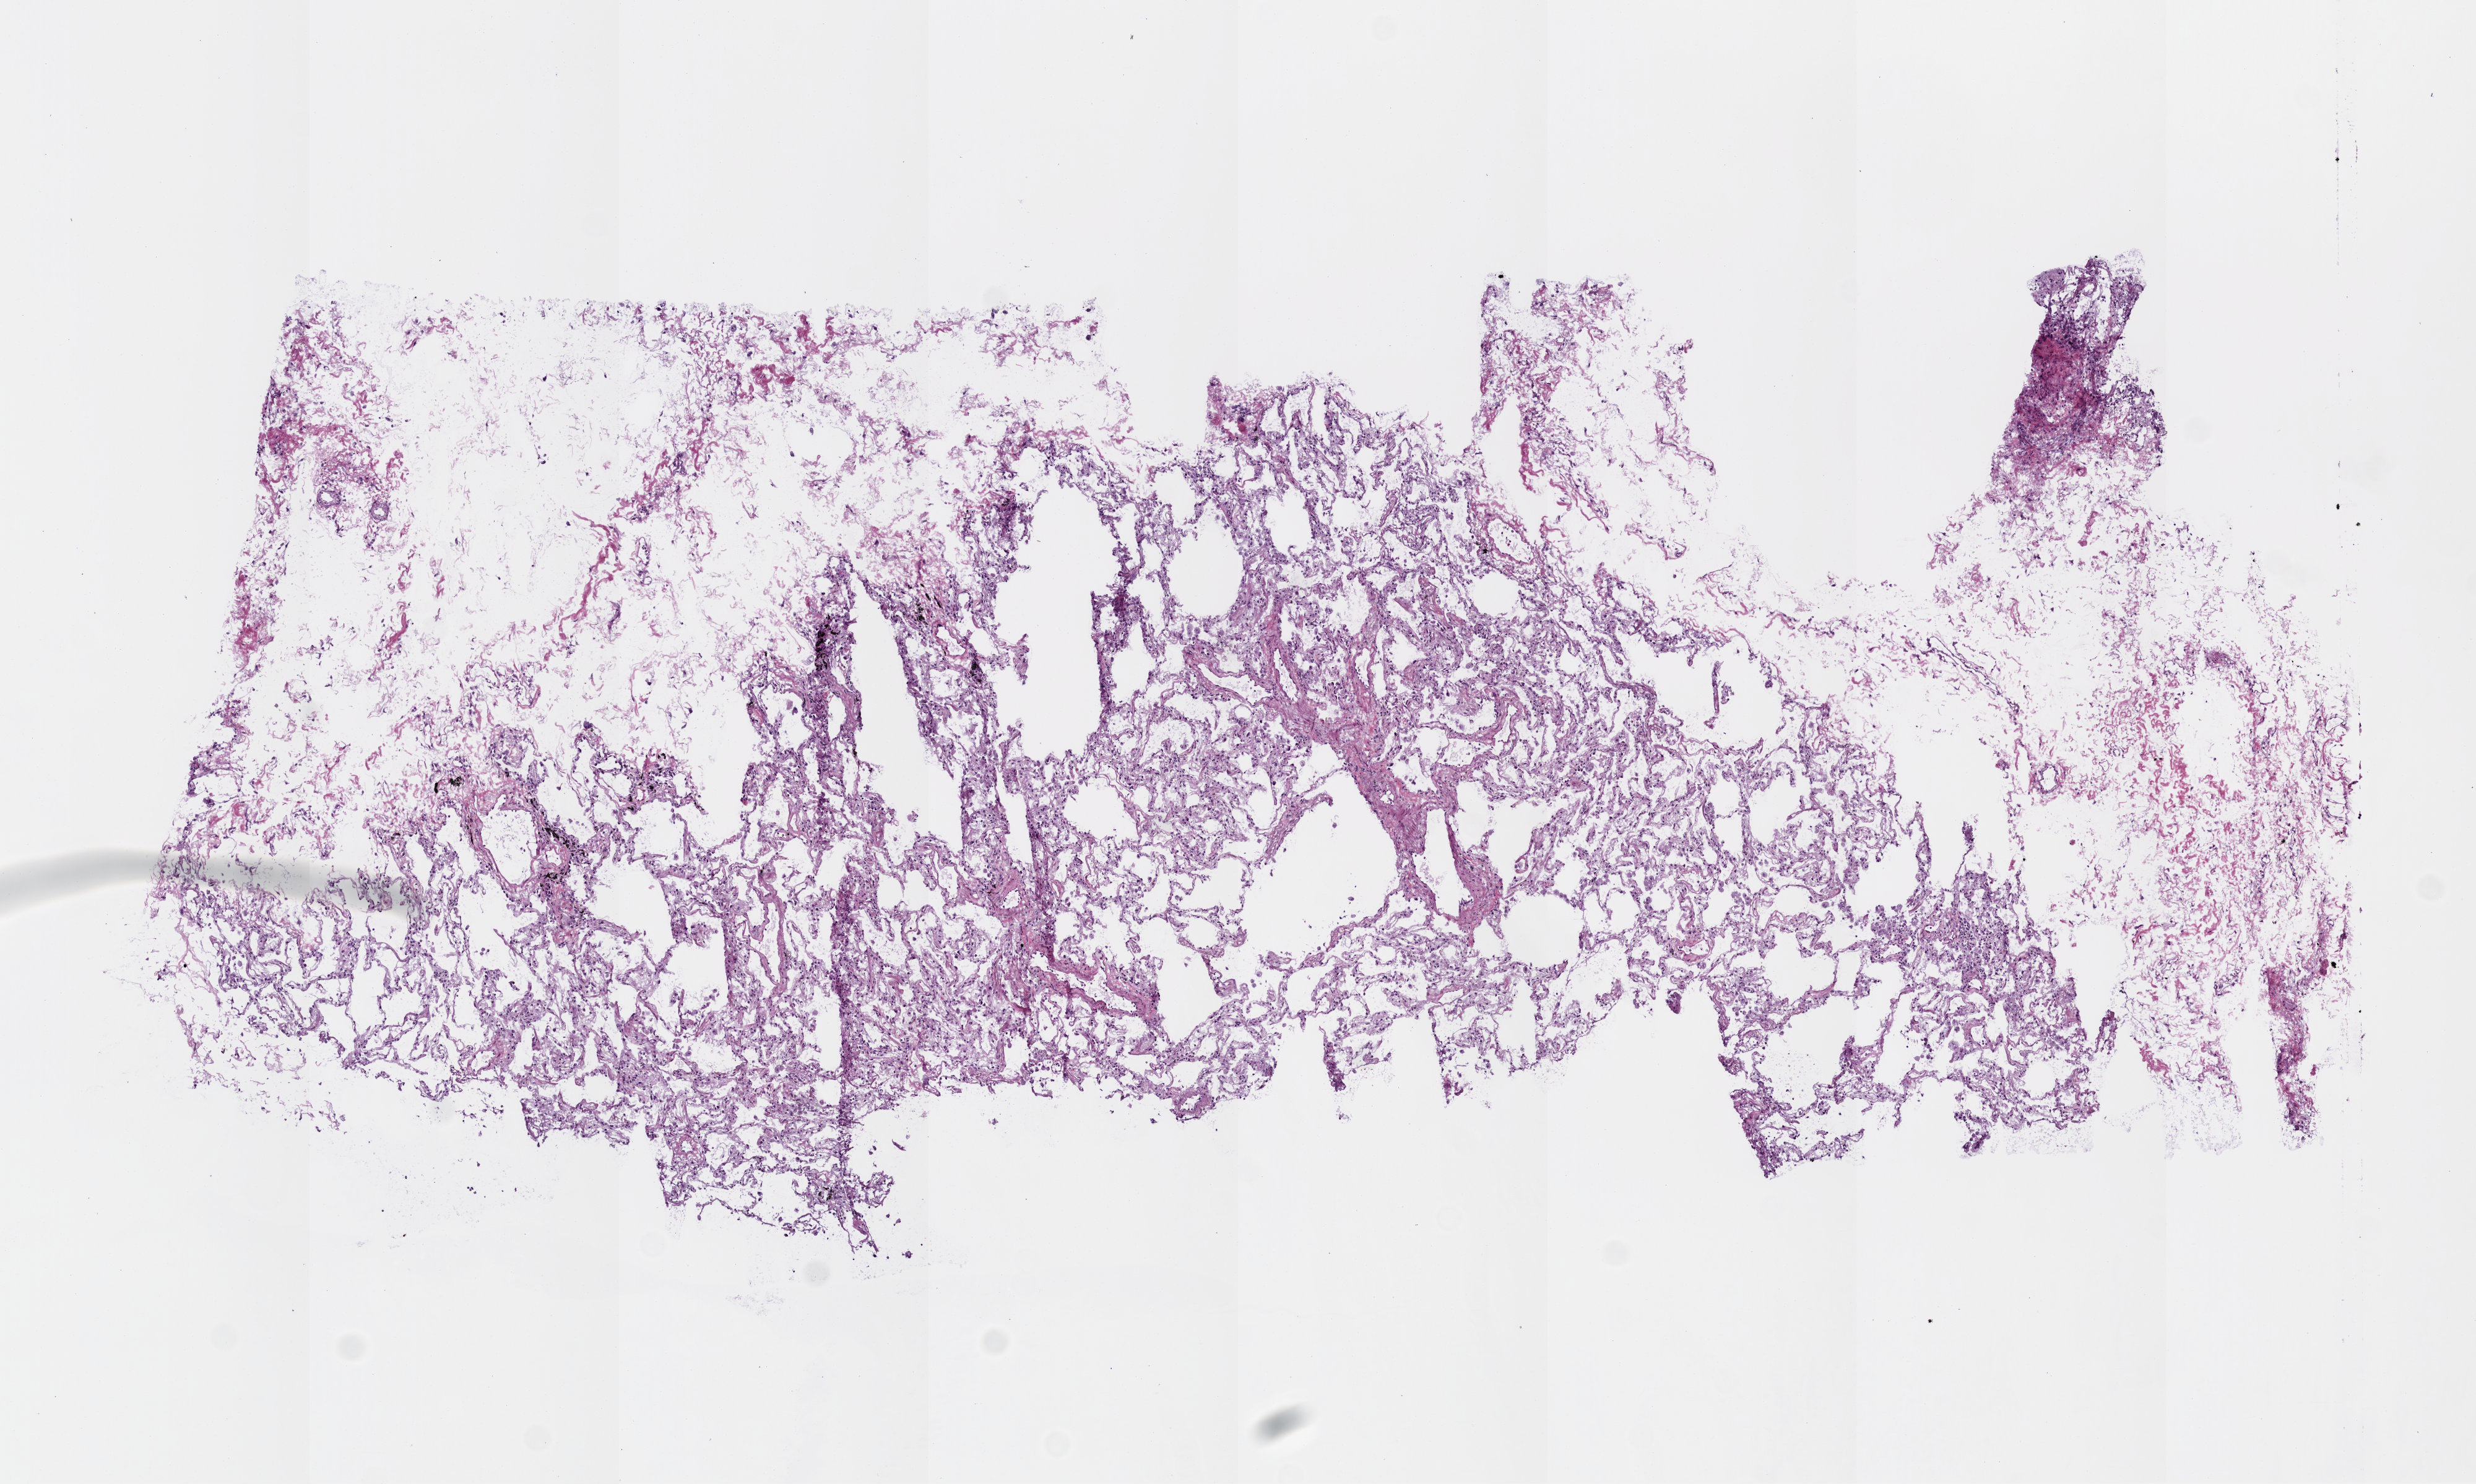
Digitized Hematoxylin and eosin (H&E) stained tissue section (whole slide) — whole scanned area (about 8.0 x 4.8 mm, acquisition: 20x scan) shown as a low-resolution overview, frozen section from the top of the tissue portion, lung, solid tissue normal (non-tumour tissue) sample. Male, age 65 years at initial diagnosis.
• this section: solid tissue normal (non-tumour) sample from the same patient
• patient diagnosis: Adenocarcinoma, NOS